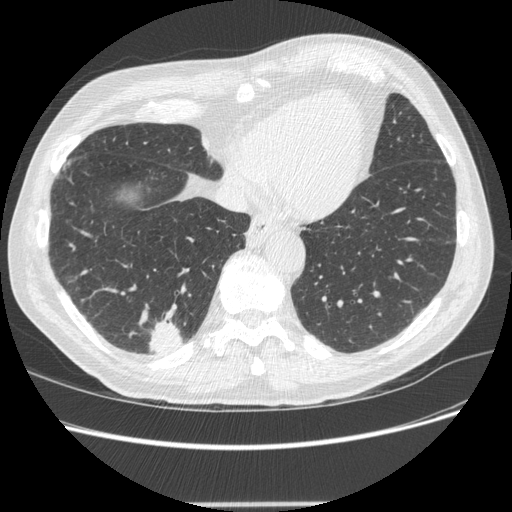
Low-dose screening chest CT, one axial slice; slice 65 of 245 in the series (ordered by position); 120 kVp; lung window (W 1500 / L -600 HU); 1.25 mm slice thickness; 512 × 512 image matrix, field of view 372 × 372 mm.
Annotated regions visible in this slice (expert manual segmentation):
- lesion 1 (tumor, lower lobe of right lung): bounding box (x1, y1, x2, y2) in pixels: (148, 320, 183, 353)